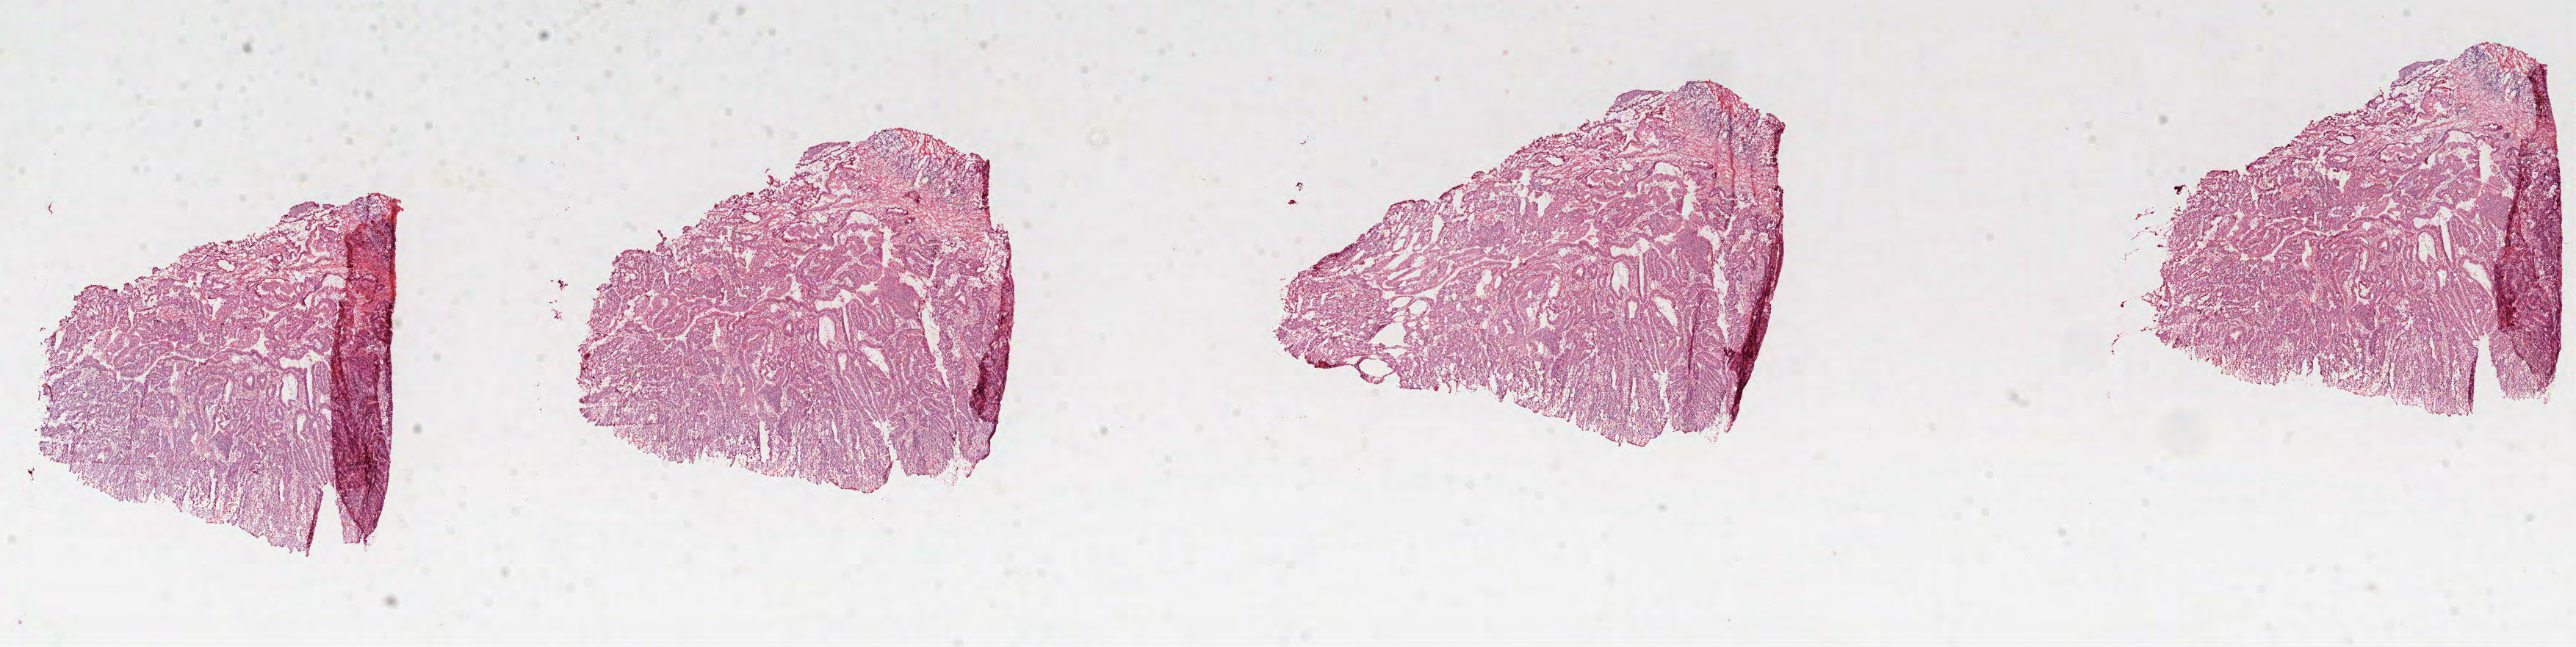
Digitized H&E tissue section (whole slide) — whole scanned area (about 28.3 x 7.1 mm, acquisition: 40x scan) shown as a low-resolution overview, FFPE section, sample: primary tumour, colon. Female patient; age at initial diagnosis 79 years.
Histologic diagnosis: Mucinous adenocarcinoma (cecum).